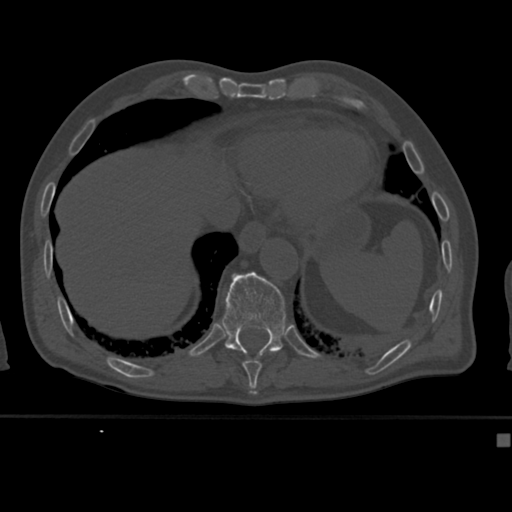
CT including the spine, one axial slice; slice 218 of 430 in the series (ordered by position); reconstruction kernel Br40s; bone window (W 1800 / L 400 HU); 1.5 mm slice thickness; 512 × 512 image matrix, field of view 337 × 337 mm. Patient: male, 64 years. Case-level facts recorded for this patient, not image findings: primary cancer: uterus.
Outlined on this slice (semi-automatic segmentation, software-assisted and operator-edited):
- T10 vertebra: bounding box <242,356,262,382> (left, top, right, bottom; pixels)
- T11 vertebra: <222,271,286,356>